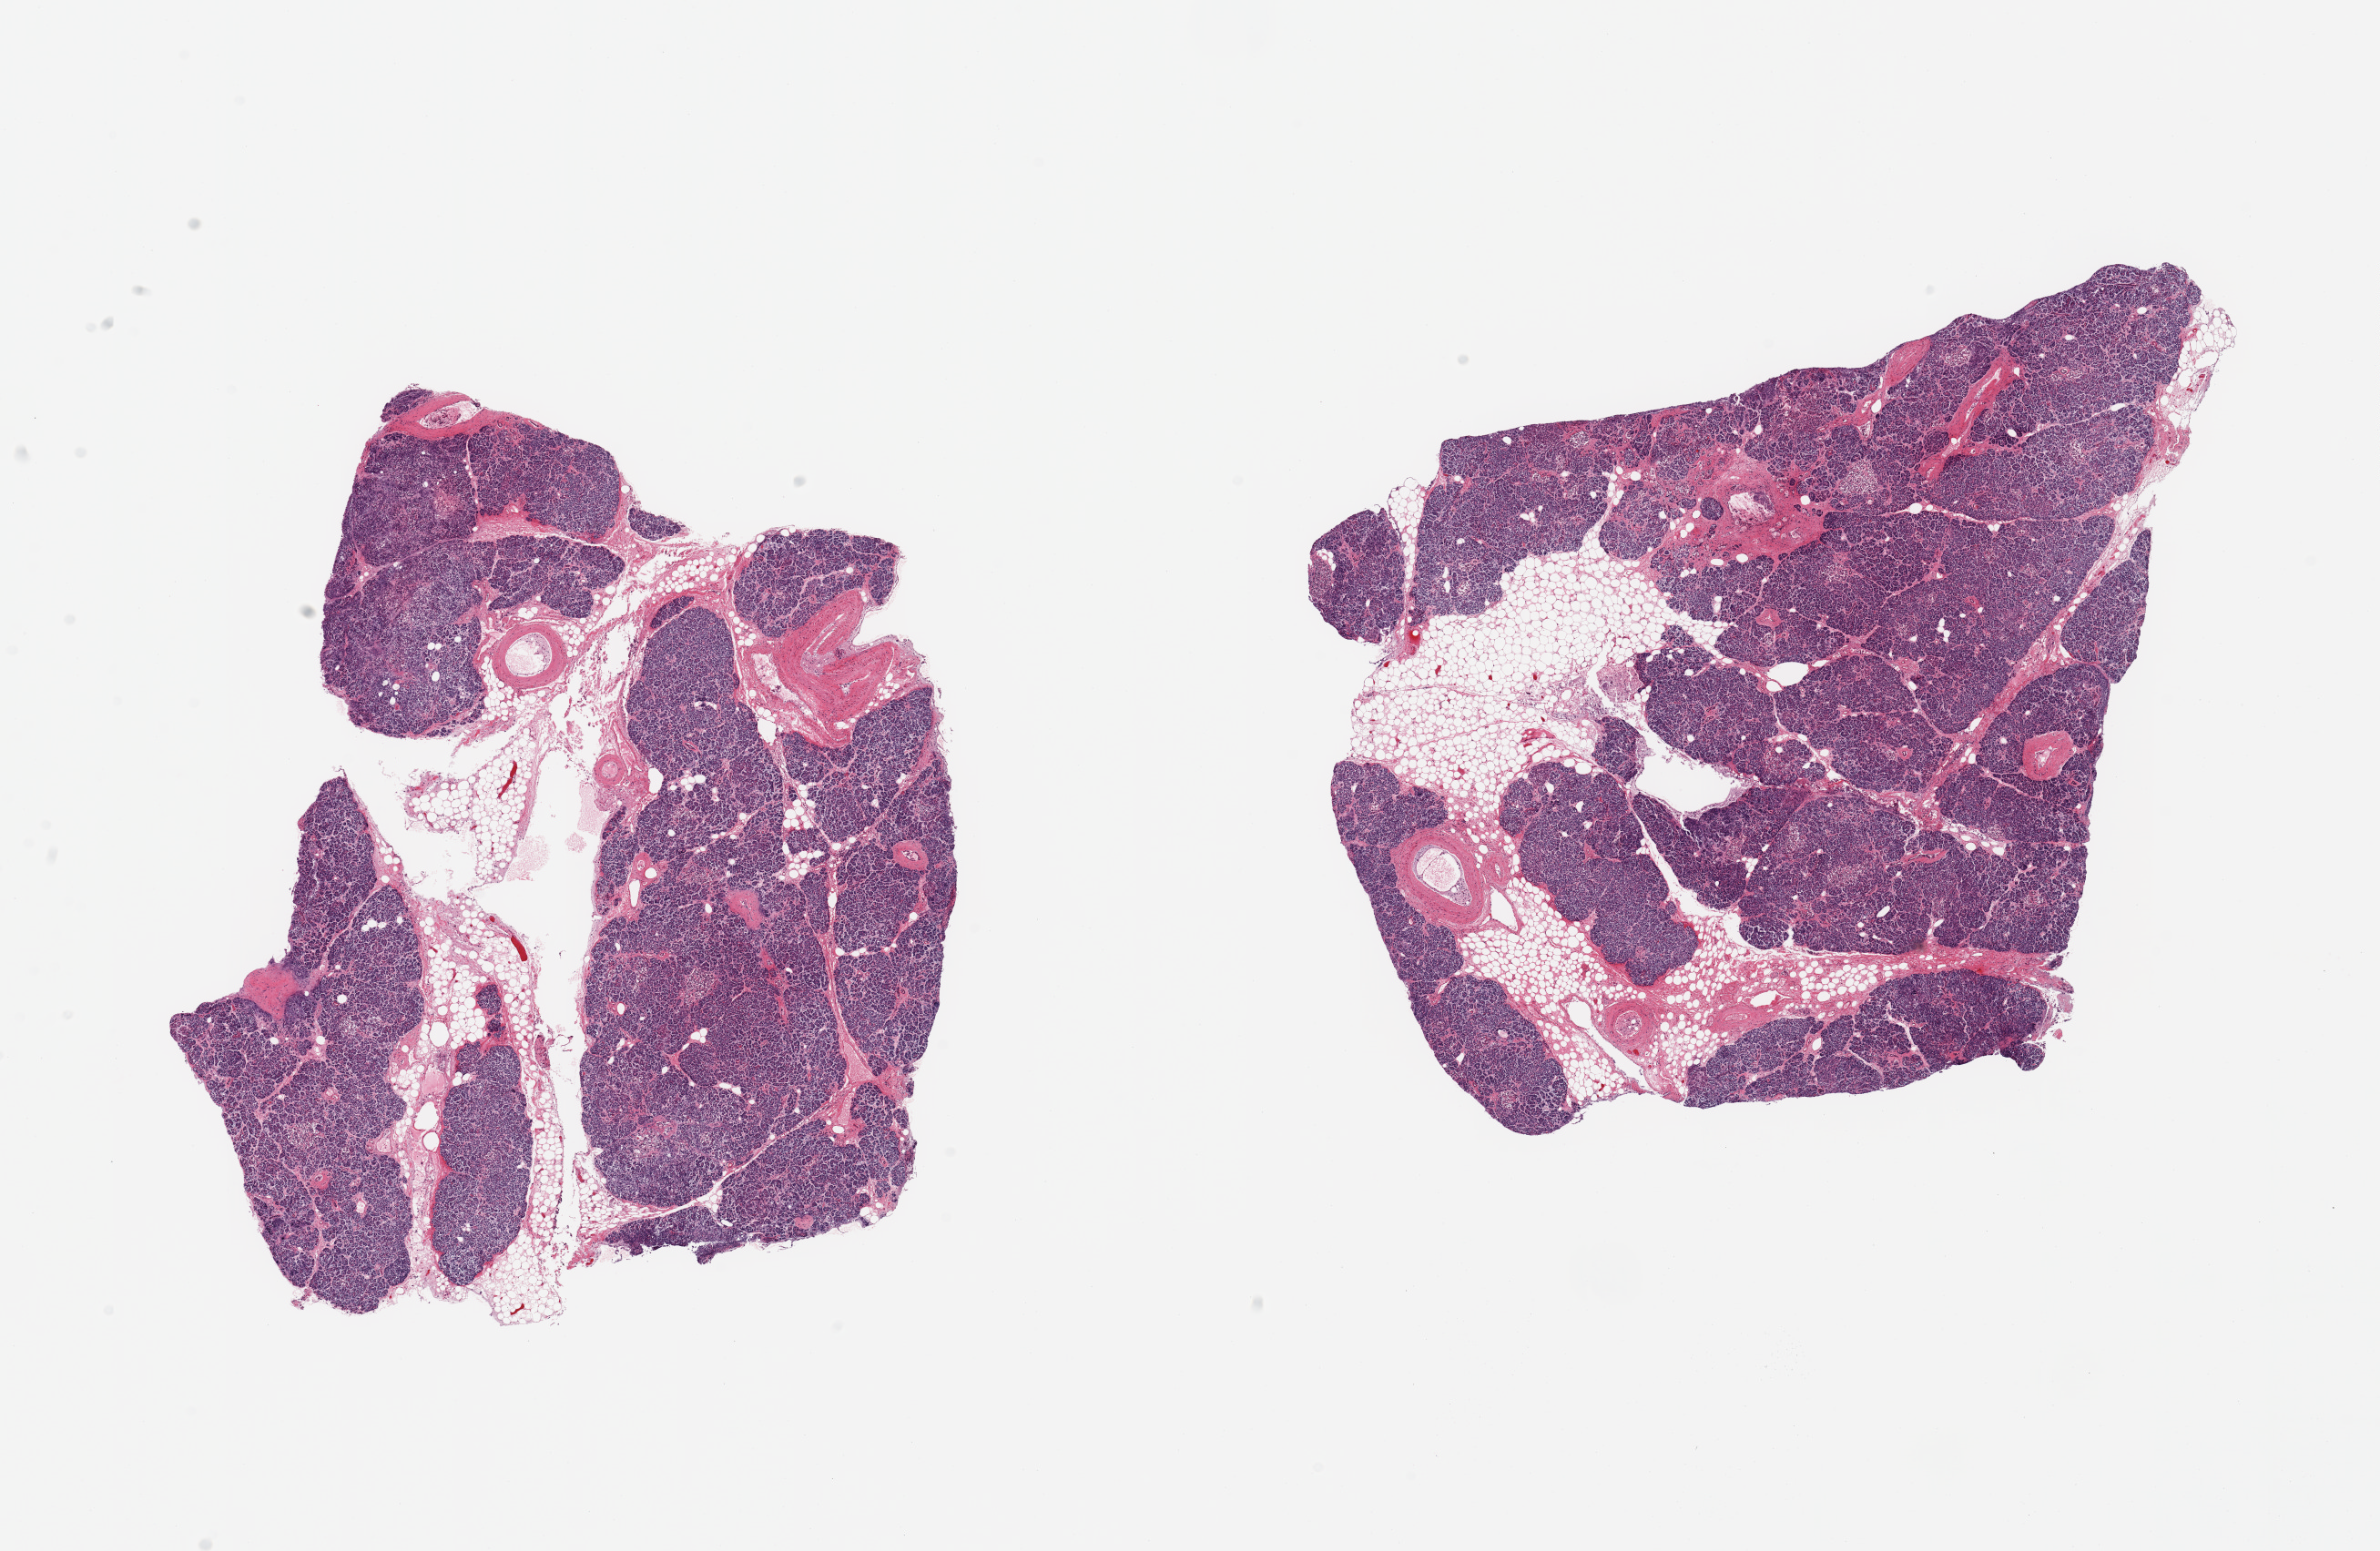
H&E whole-slide image, whole scanned area (about 20.7 x 13.5 mm, acquisition: 20x scan) shown as a low-resolution overview. PAXgene-fixed, paraffin-embedded tissue. Sampled site (target tissue): pancreas. Donor tissue sample.
• review note (as recorded): 2 pieces; 10-20% internal fat